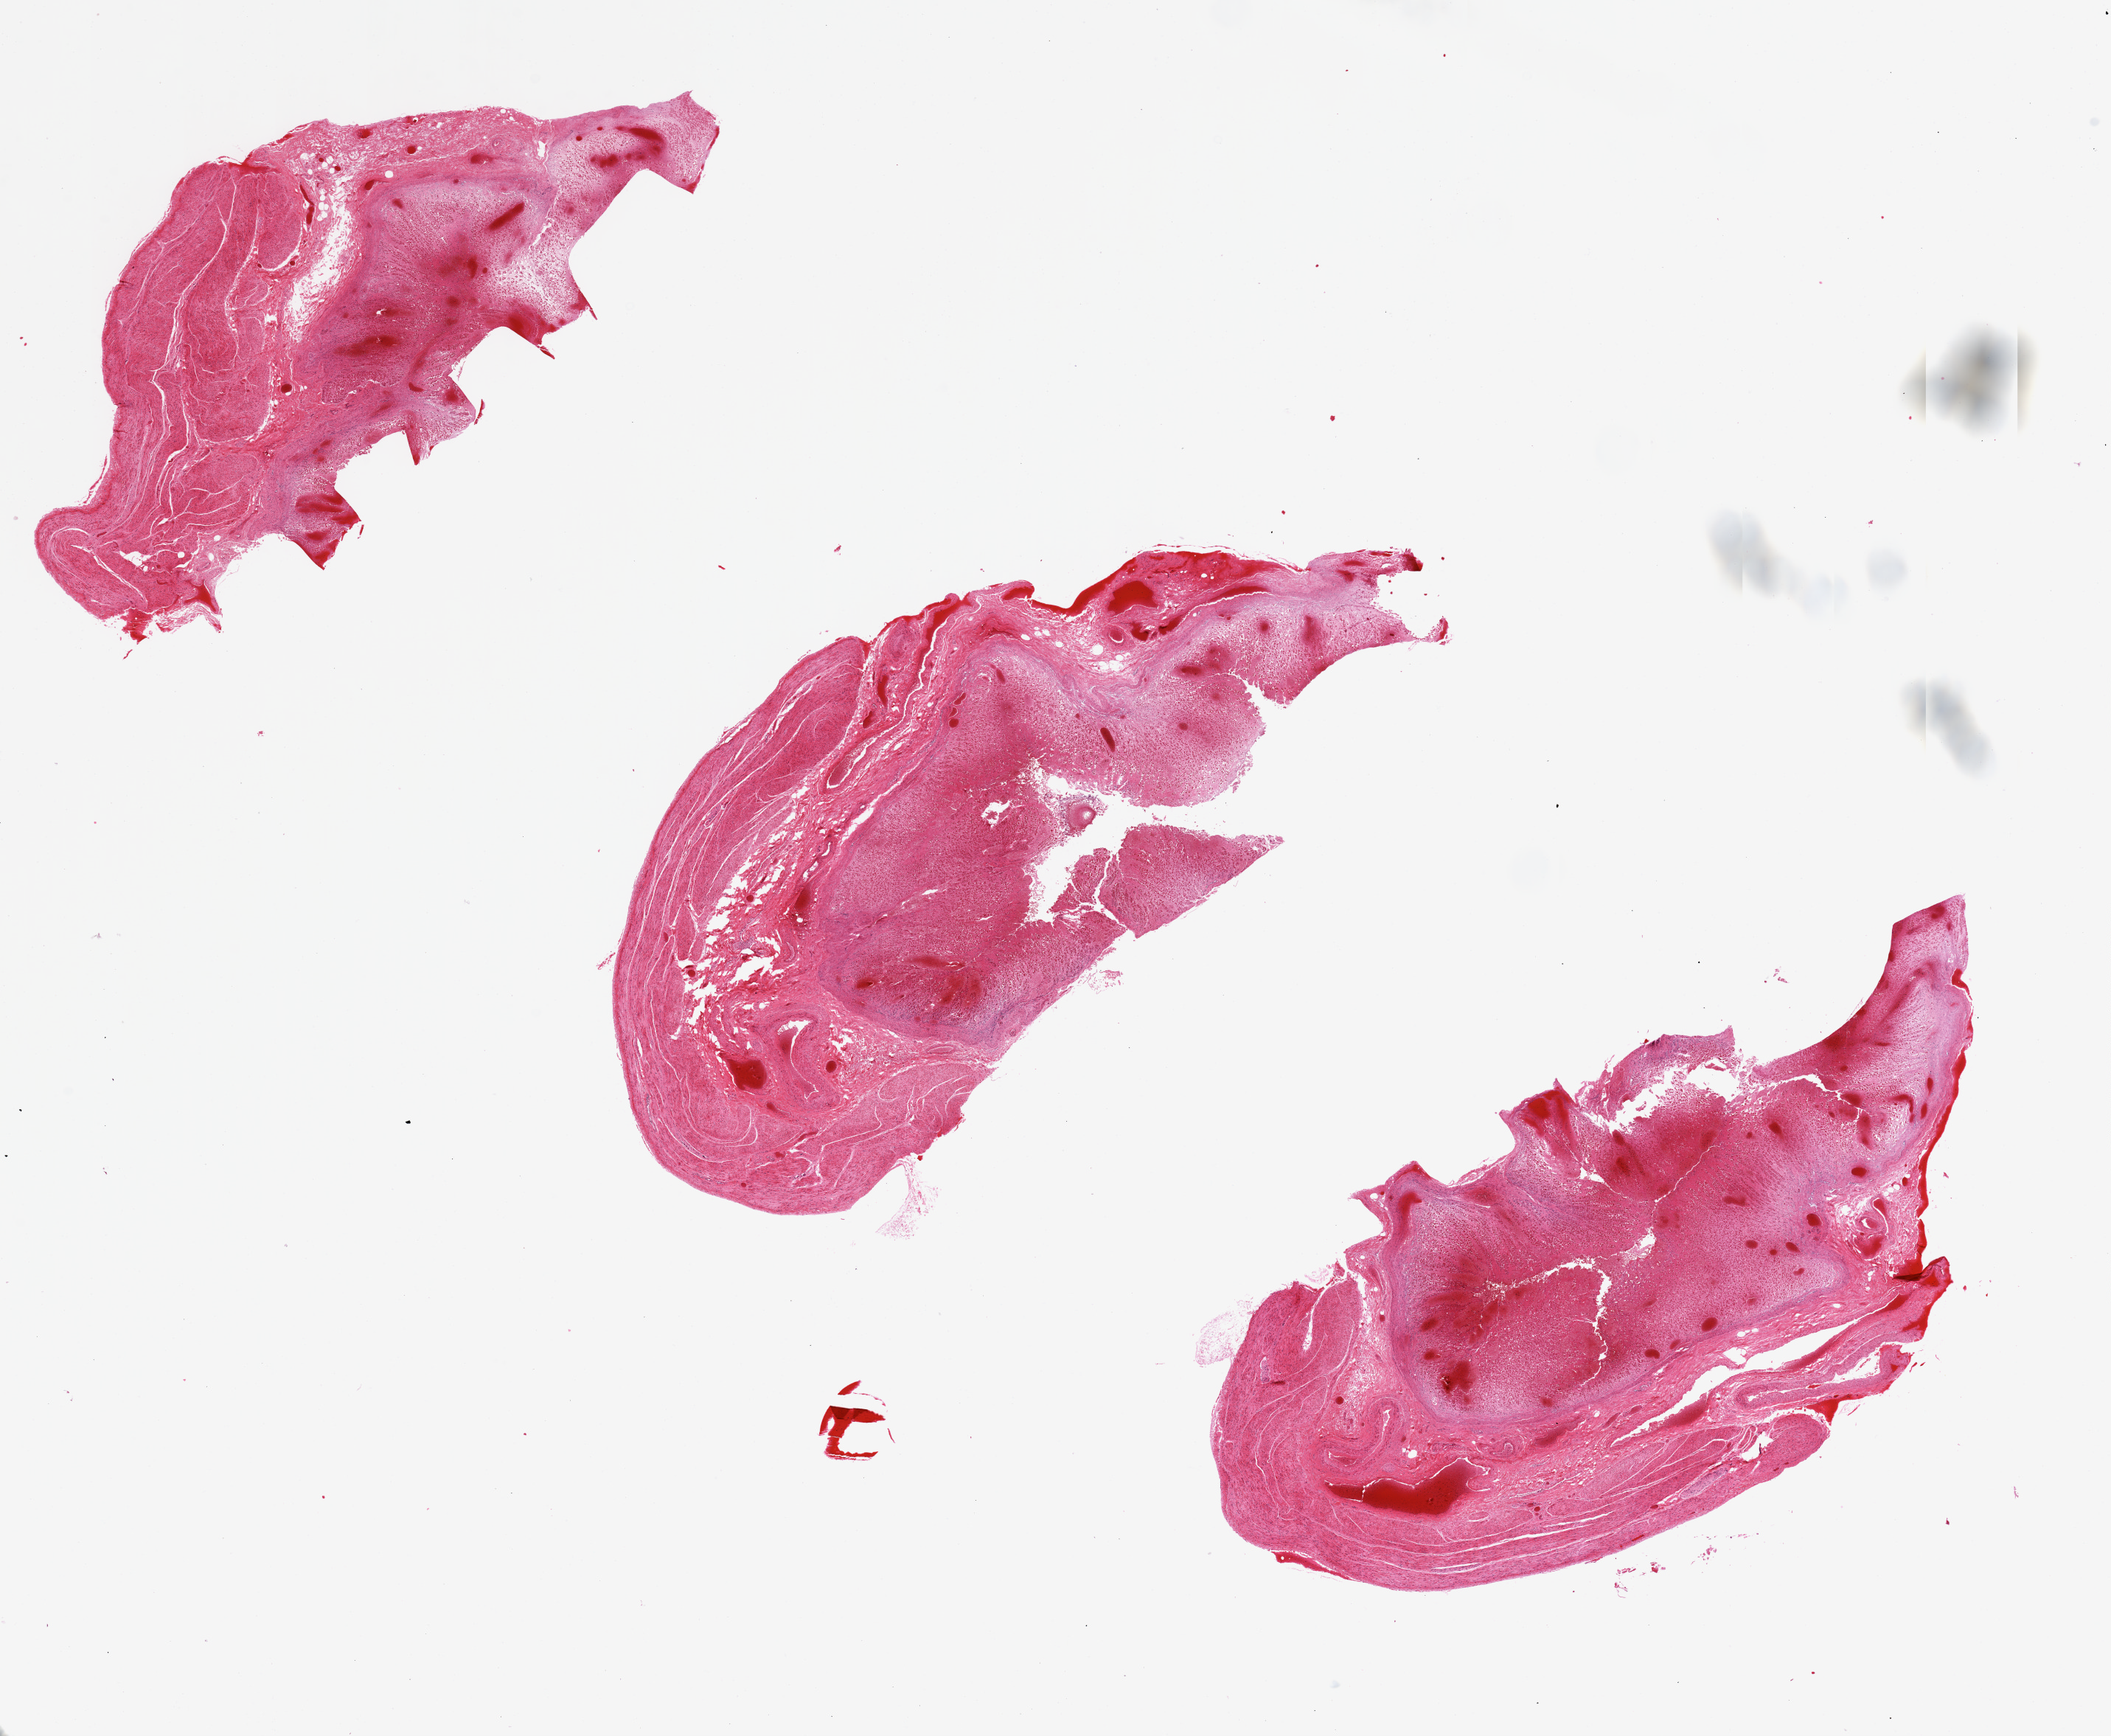
Haematoxylin and eosin whole-slide image, brightfield, a low-resolution overview of the entire scanned area, about 22.6 x 18.6 mm (acquisition: 20x scan), PAXgene-fixed paraffin-embedded (PFPE) section, target tissue: stomach, donor tissue sample. Donor: male.
Pathologist's review note for this sample: 3 pieces up to 10x5 mm. Glands 100% autolyzed.